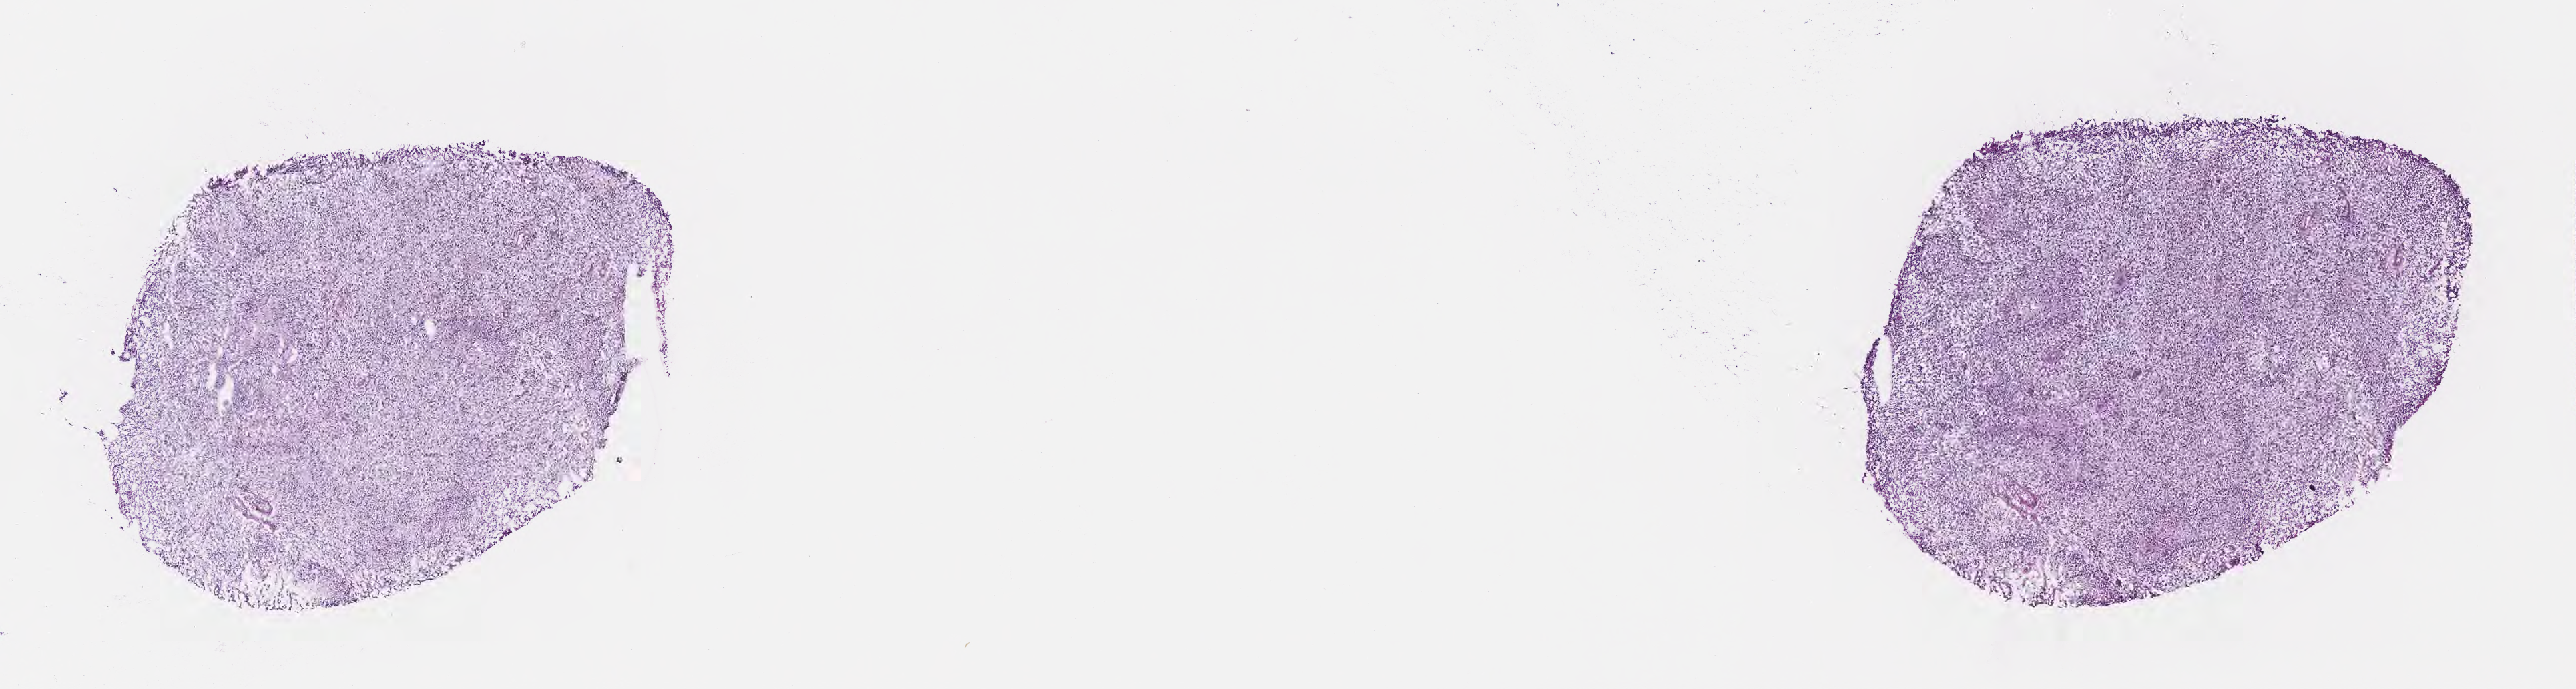
Haematoxylin and eosin whole-slide image — shown as a low-resolution overview of the whole scanned area (about 15.6 x 4.2 mm). Frozen section. Primary tumor. Anatomic site: brain. Patient: female, age at initial diagnosis 82 years. Slide review estimates, as recorded: tumor cells 89%, tumor nuclei 96%, stromal cells 2%, necrosis 5%, normal cells 4%. Infiltration values recorded for this section: lymphocyte infiltration 0%, monocyte infiltration 0%, neutrophil infiltration 0%.
* histologic diagnosis: Glioblastoma, NOS